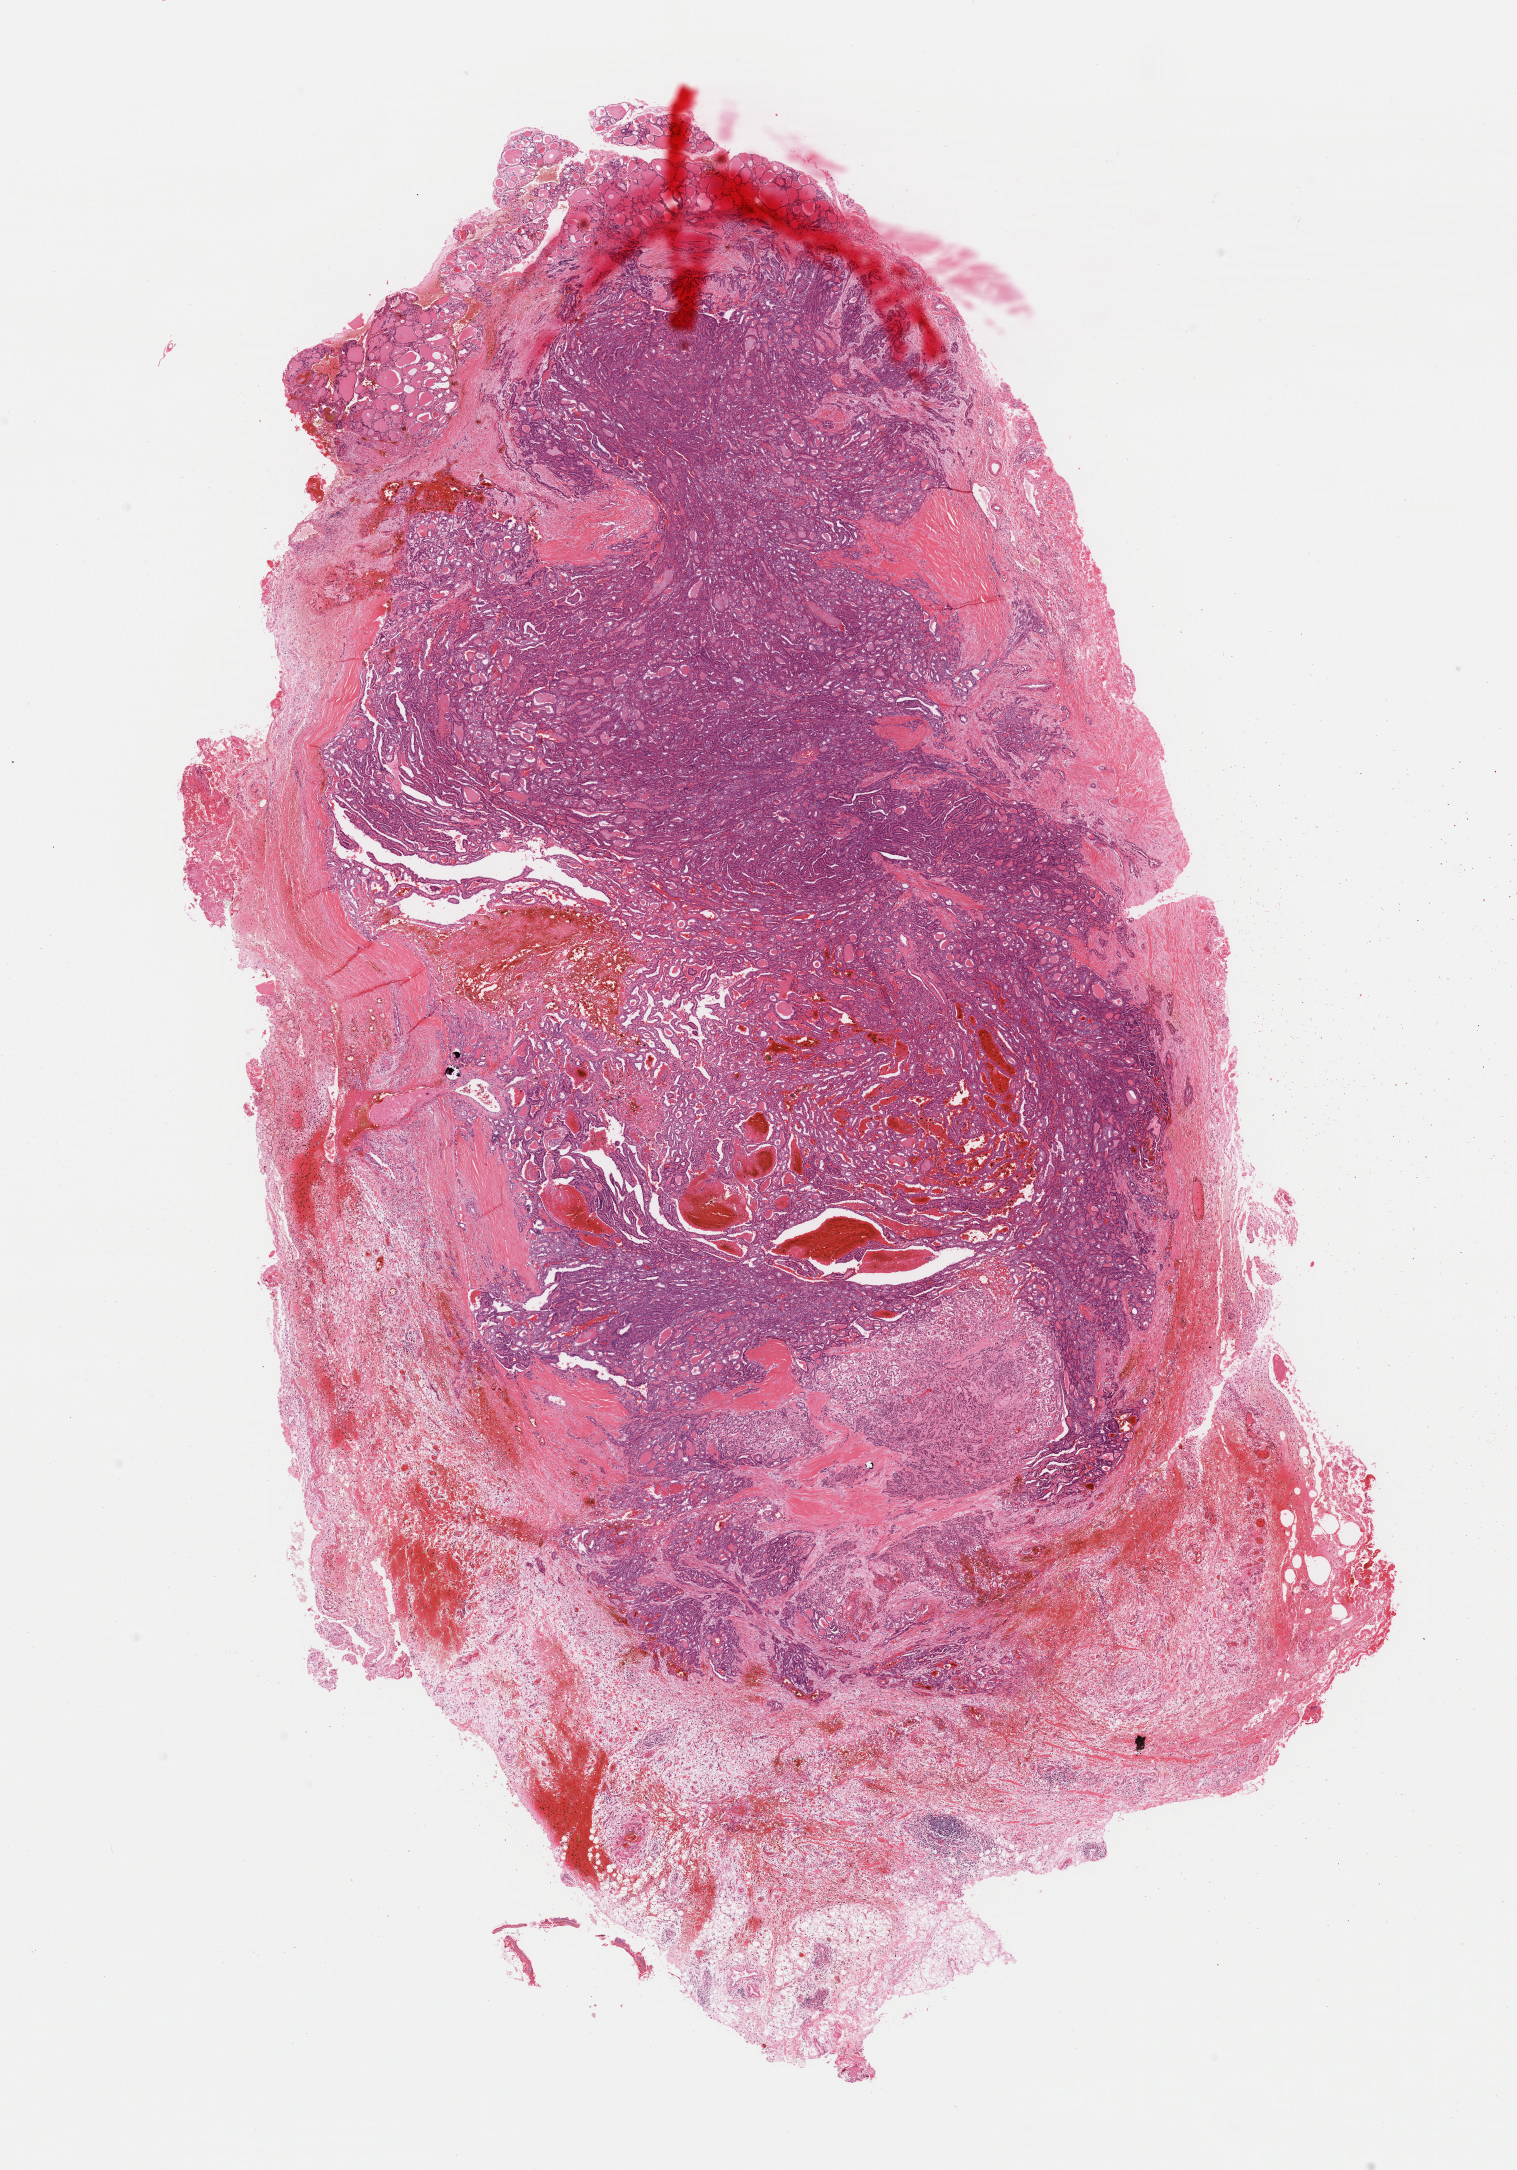
Hematoxylin and eosin (H&E) stained whole-slide image — whole scanned area (about 12.0 x 17.1 mm) shown as a low-resolution overview. Formalin-fixed paraffin-embedded (FFPE) diagnostic section. Sample: primary tumour, thyroid. Female patient; age at initial diagnosis 38 years.
TNM: T1b N0 M0. AJCC pathologic stage: I (7th edition). Diagnosis: Papillary adenocarcinoma, NOS (thyroid gland).